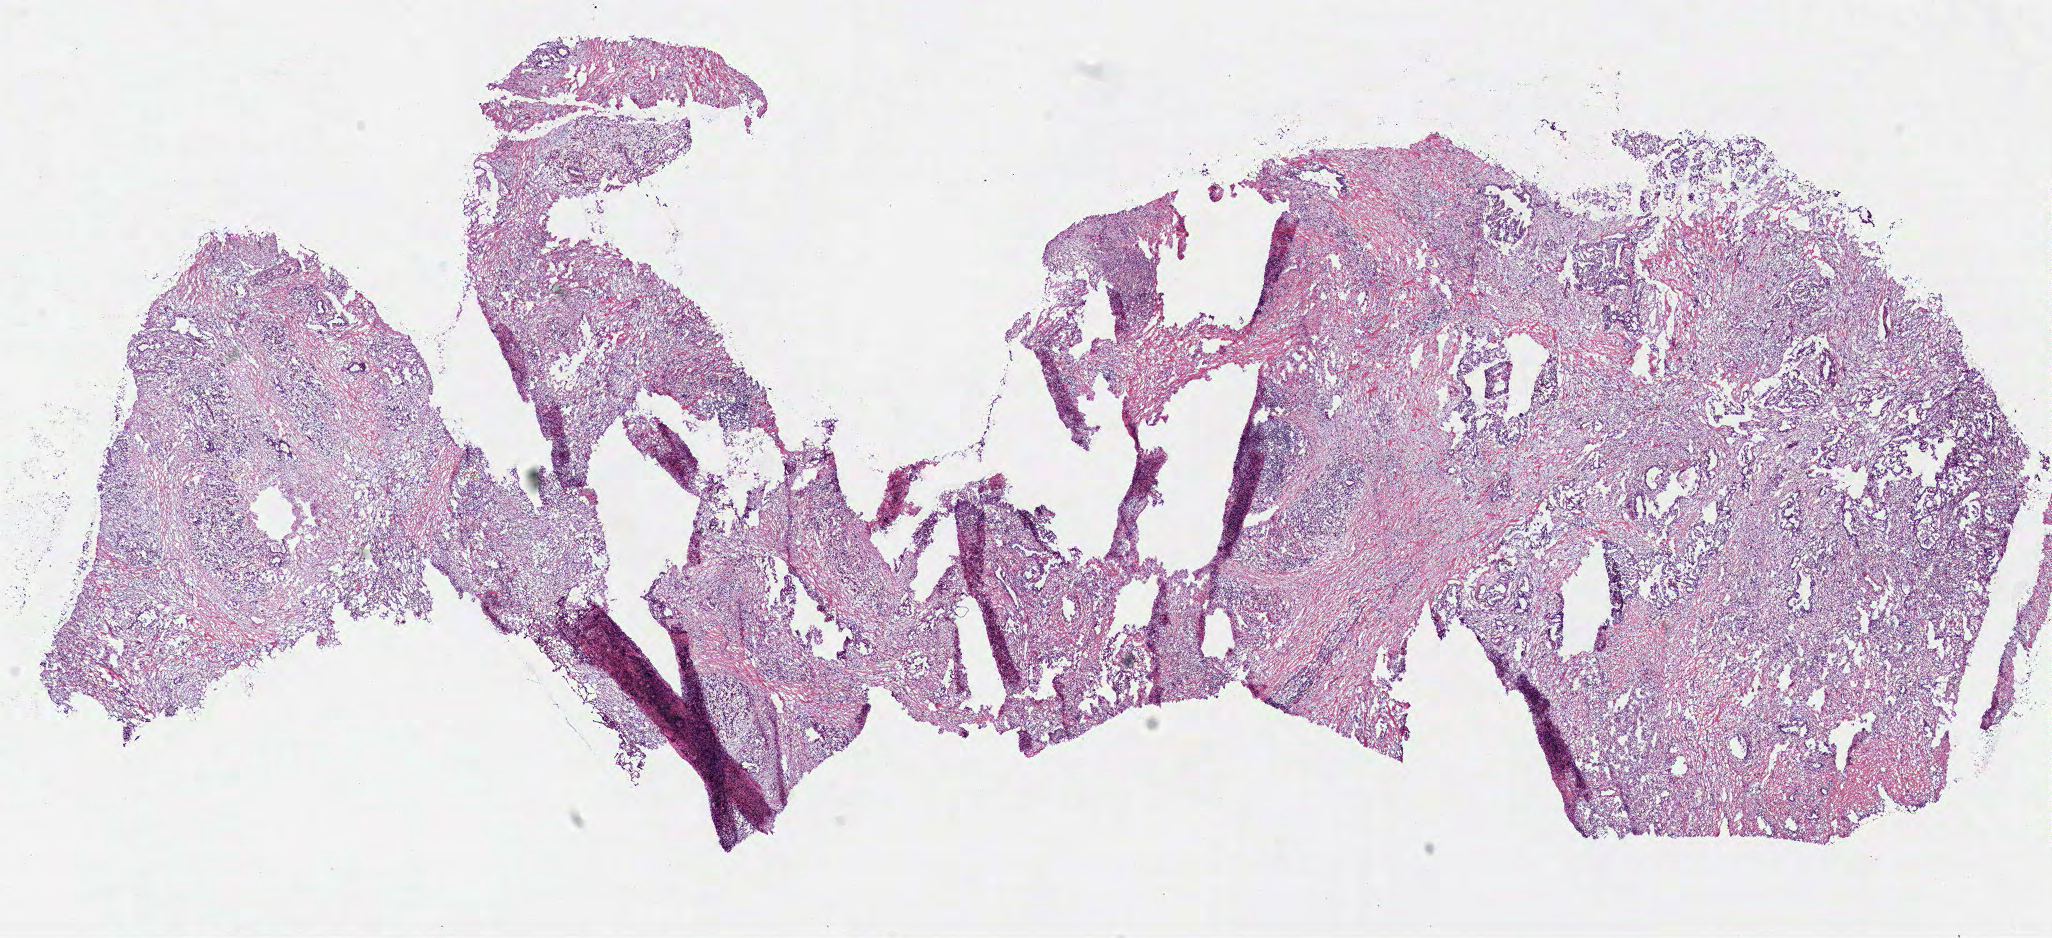
H&E-stained whole-slide image — whole scanned area (about 16.2 x 7.4 mm, acquisition: 40x scan) shown as a low-resolution overview; frozen section from the bottom of the tissue portion; pancreas, primary tumour sample. Patient: female, age at initial diagnosis 59 years. Histologic grade: G3 (poorly differentiated). Pathologist review of this section (percent, as recorded): tumour cells 35%, tumour nuclei 50%, normal cells 0%, stromal cells 63%, necrosis 2%. Infiltration values recorded for this section: lymphocyte infiltration 25%.
AJCC pathologic stage: IIB. Histologic diagnosis: Infiltrating duct carcinoma, NOS (head of pancreas).